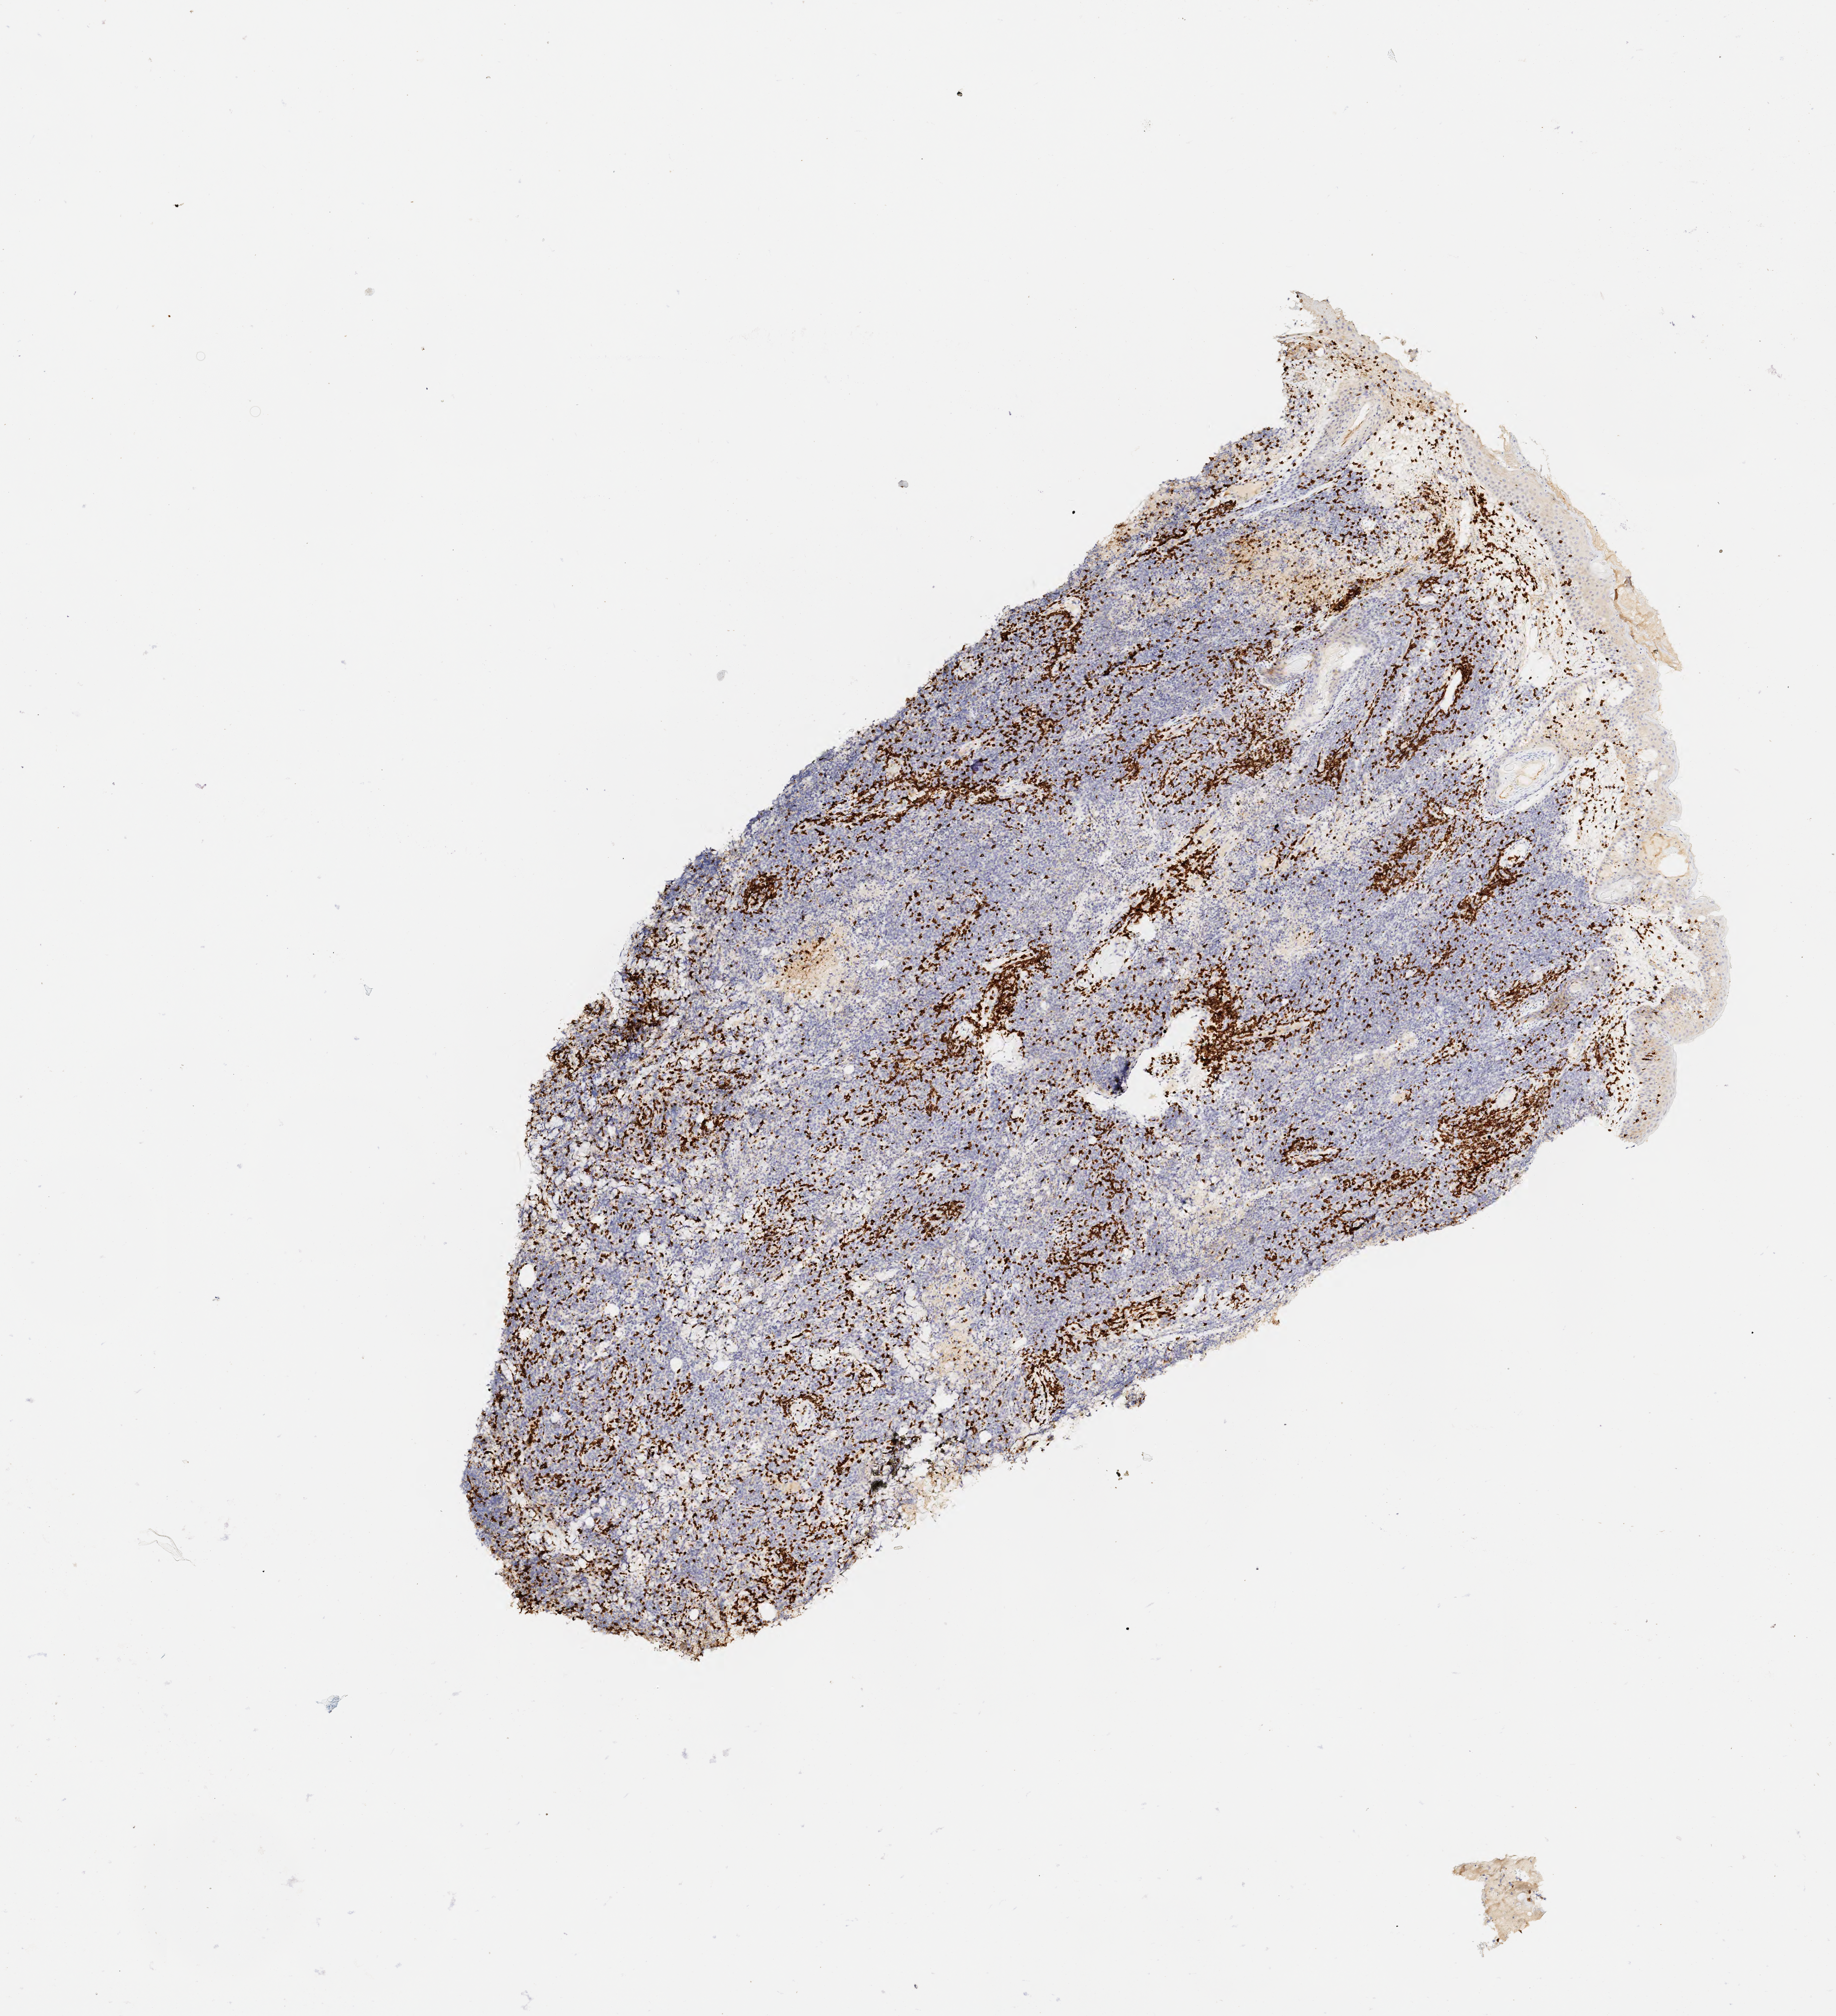
Immunohistochemistry (IHC) whole-slide image stained for CD3 — whole scanned area (about 5.5 x 6.1 mm) shown as a low-resolution overview, tumor tissue. Male patient, aged 41.
Histologic diagnosis: Diffuse large B-cell lymphoma, NOS.